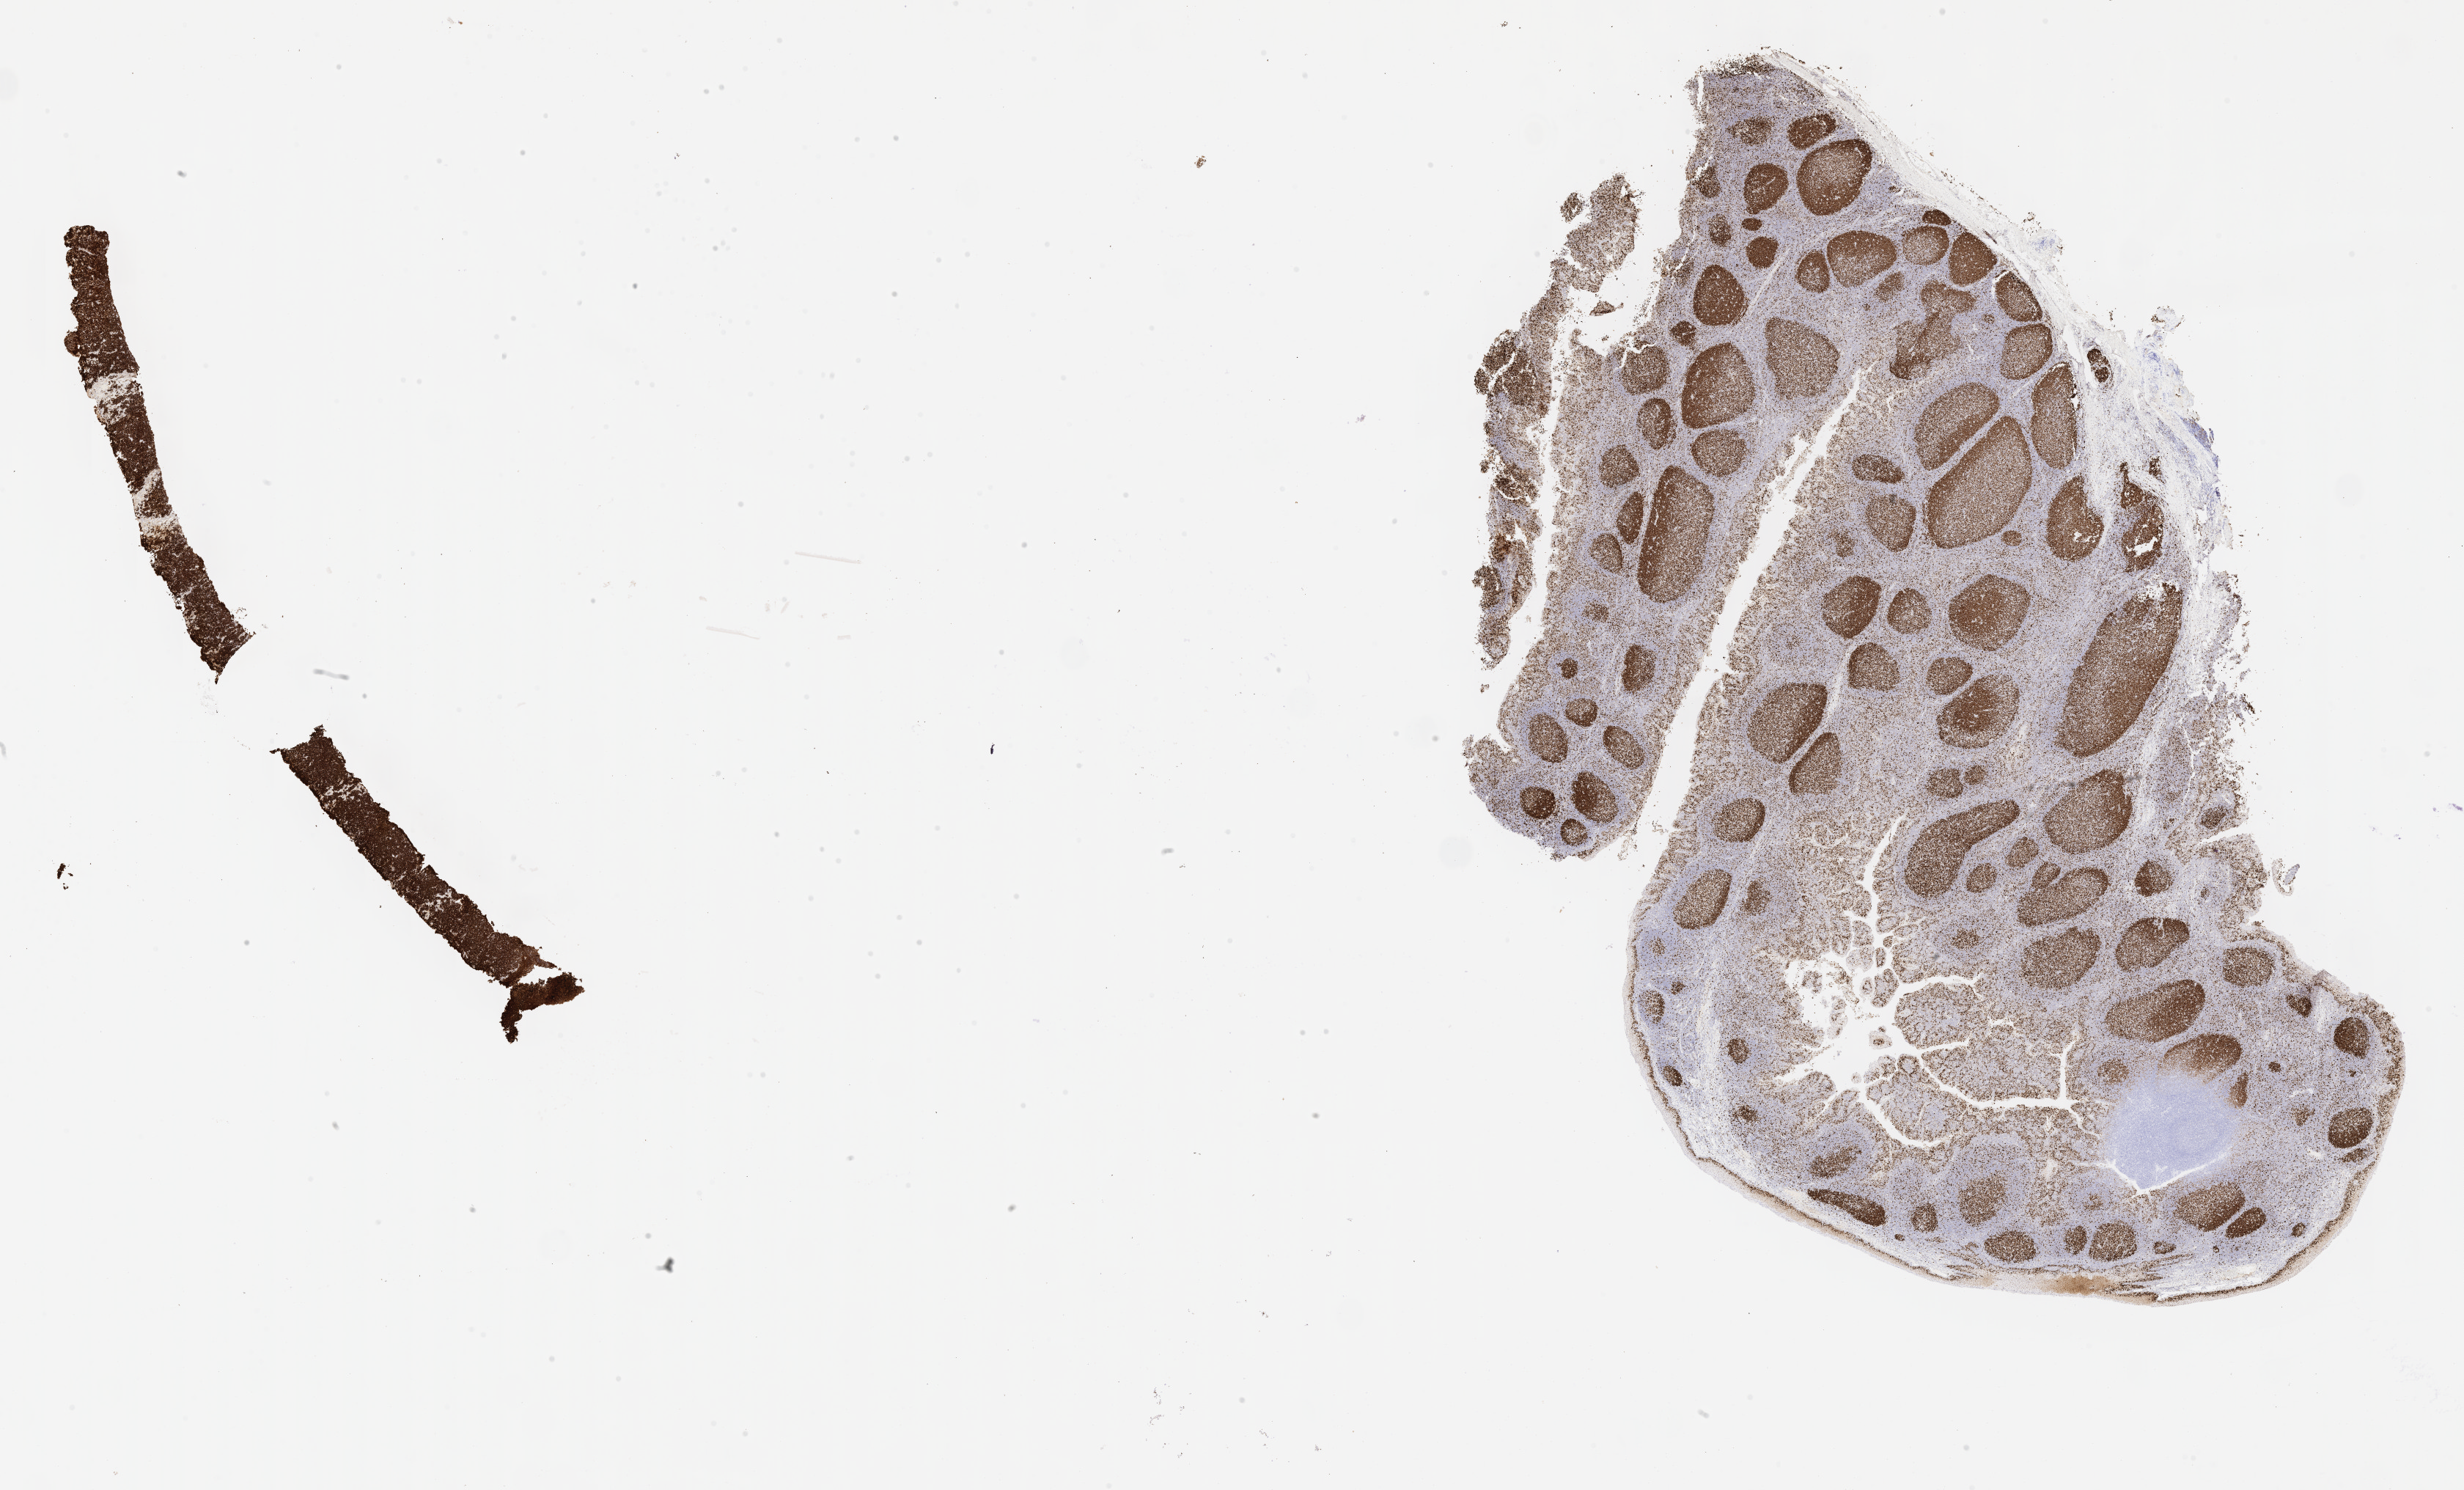
Immunohistochemistry (IHC) whole-slide image stained for Ki-67, shown as a low-resolution overview of the whole scanned area (about 27.2 x 16.4 mm). Female patient.
Specimen: tumor tissue.